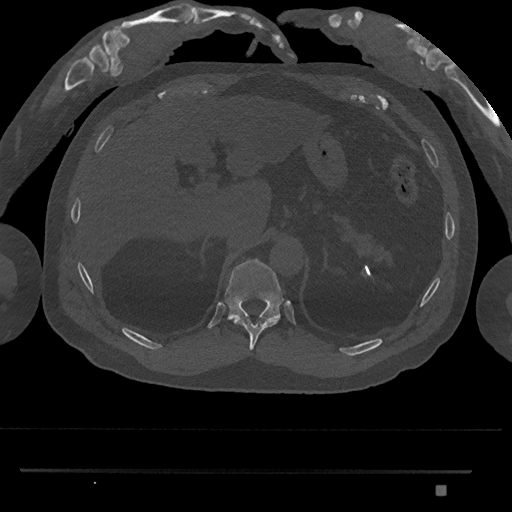
CT including the spine, one axial slice. Reconstruction kernel Br40s/3. 120 kVp. Bone window (W 1800 / L 400 HU). 0.5 mm slice thickness. 512 × 512 image matrix, field of view 429 × 429 mm. Male patient, age 65 years. From the clinical record (not read from this slice): primary cancer: prostate.
Annotated regions visible in this slice (semi-automatically segmented with operator editing):
- T10 vertebra: bounding box (x1, y1, x2, y2) in pixels: (234, 318, 278, 351)
- T11 vertebra: (225, 259, 284, 331)